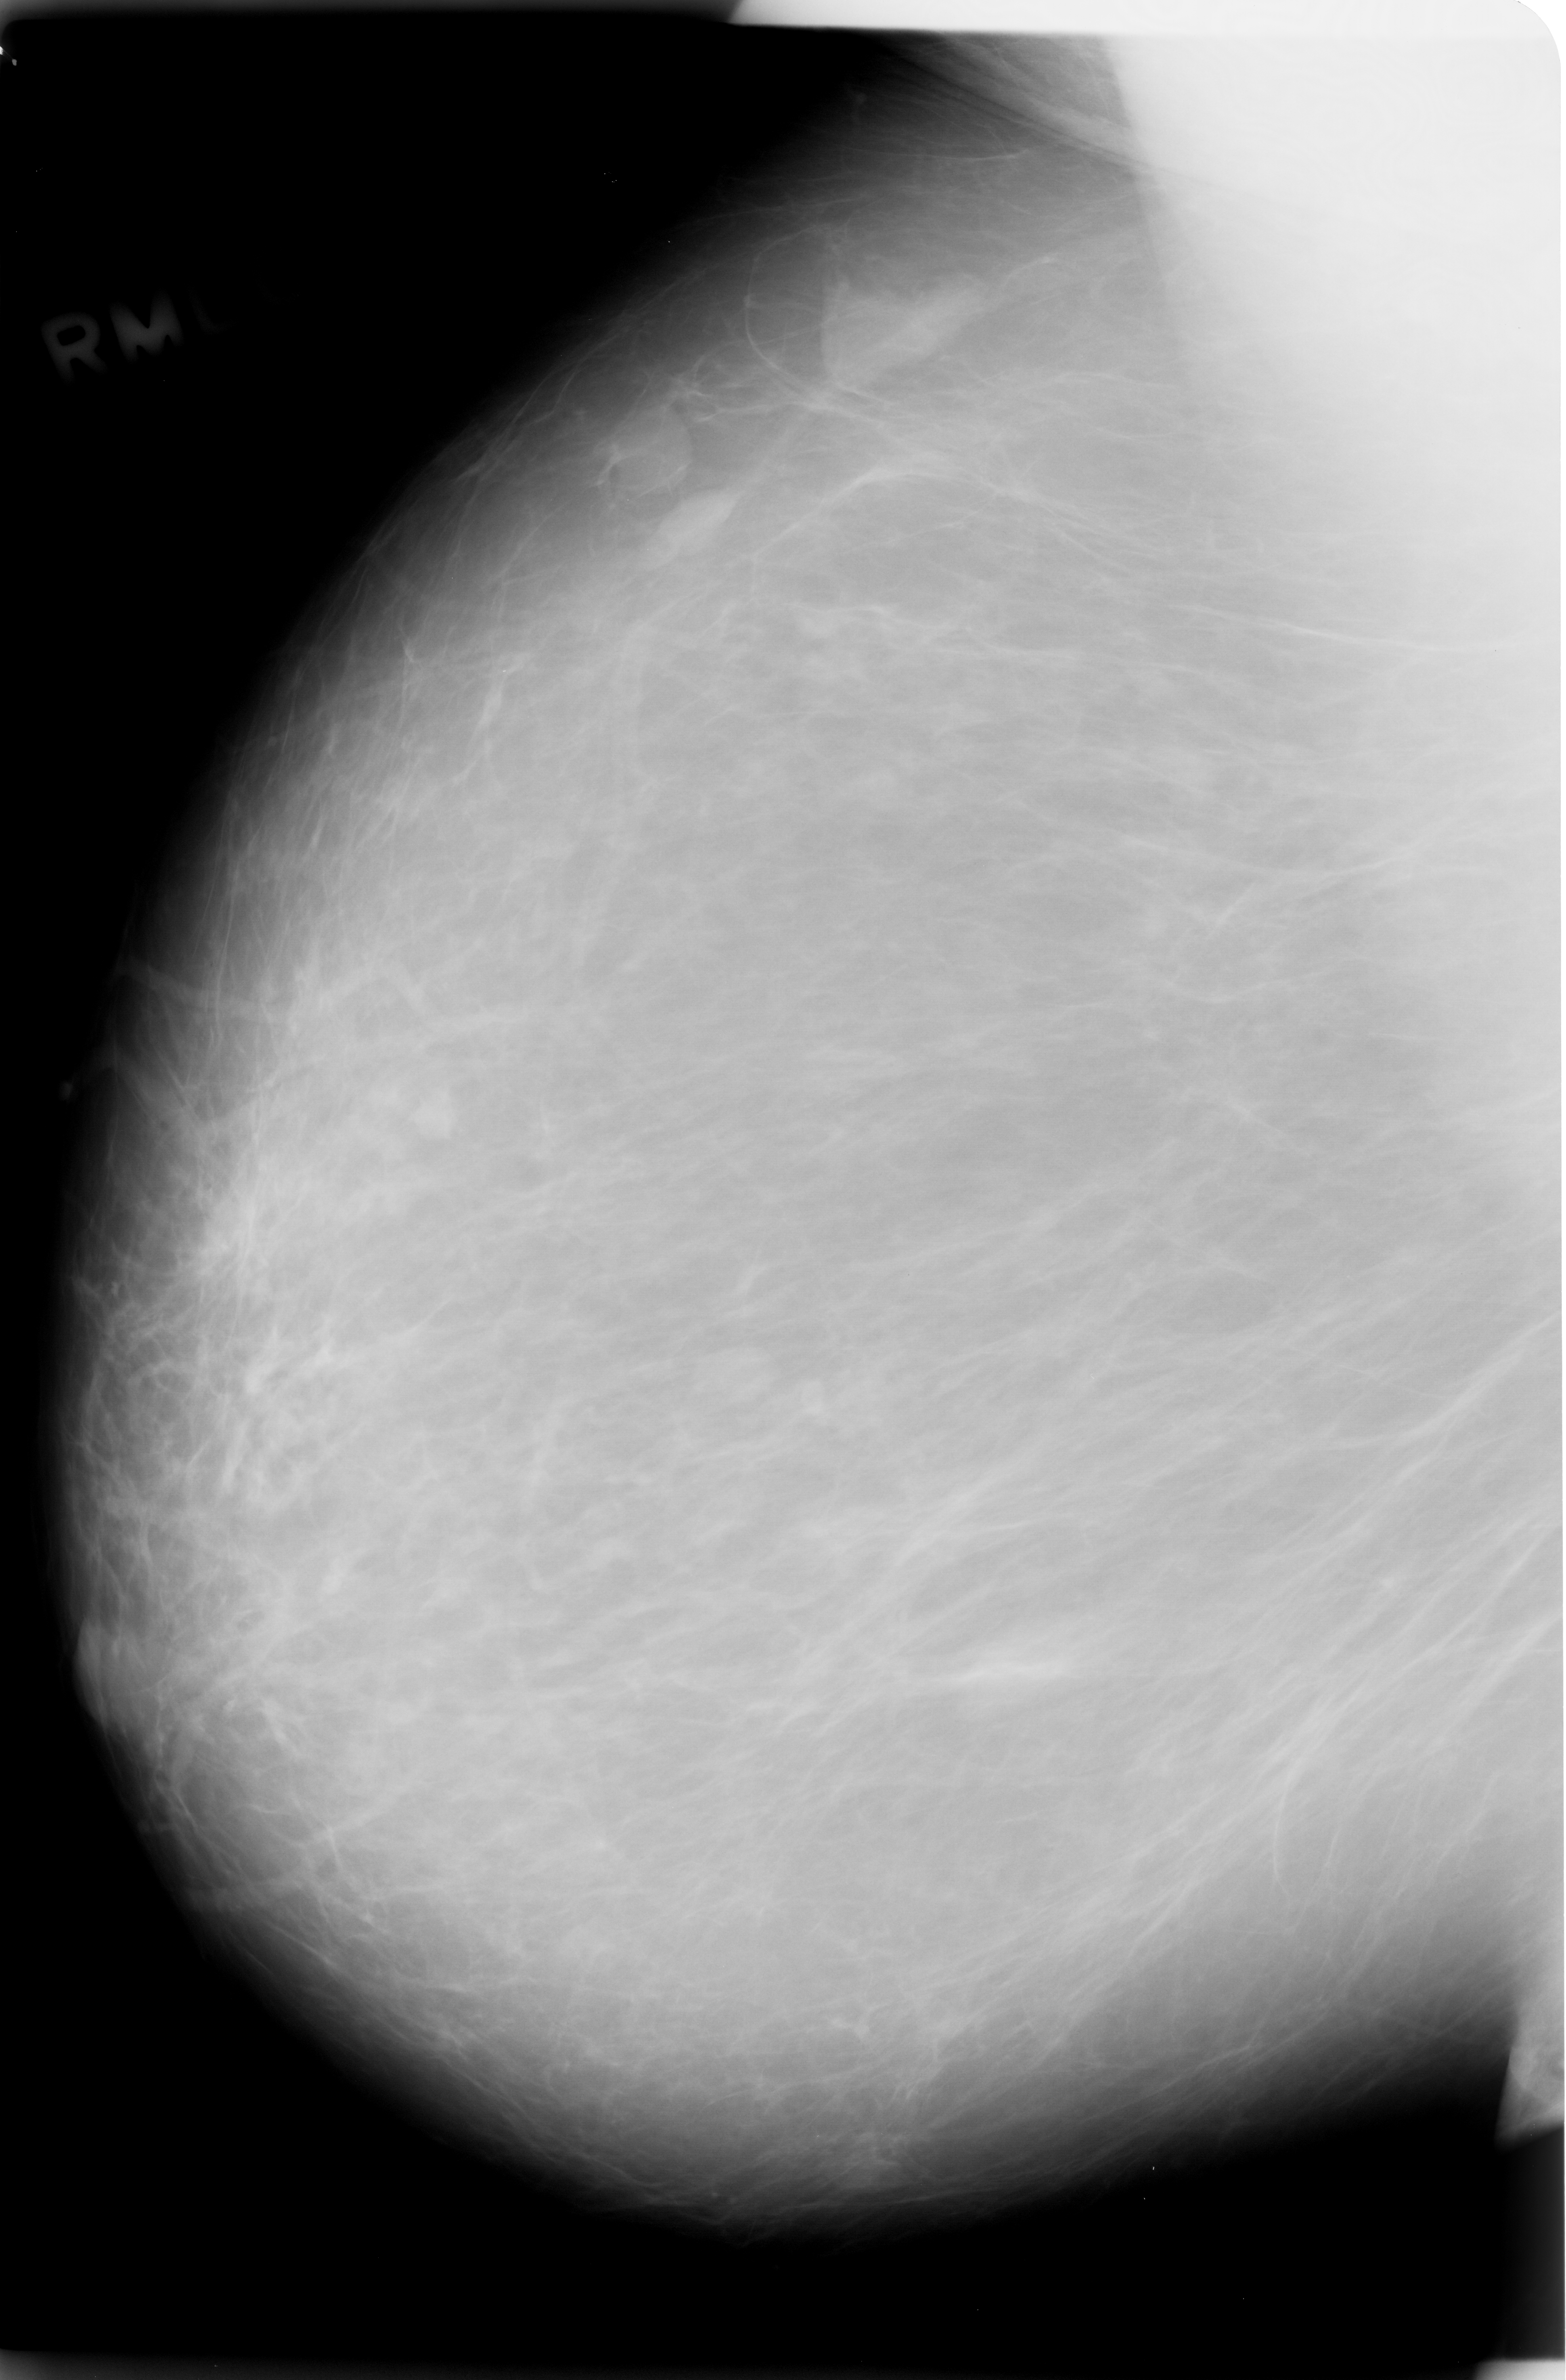
Mammogram (digitized film). Right breast. Mediolateral oblique (MLO) view. BI-RADS breast density category 1 (scale 1–4). 1566 × 2380 image matrix.
Expert-marked regions of interest on this film, with their recorded descriptors:
- Finding 1 of 6: mass, shape round, margins circumscribed; BI-RADS assessment category 2; subtlety rating 5 on a 1 (subtle) to 5 (obvious) scale; pathology (as recorded): benign: box from (x=408, y=1080) to (x=464, y=1140) px
- Finding 2 of 6: mass, shape round, margins circumscribed; BI-RADS assessment category 2; subtlety rating 5 on a 1 (subtle) to 5 (obvious) scale; pathology result (as recorded, not read from the image): benign: (x=616, y=428)–(x=741, y=568)
- Finding 3 of 6: mass, shape round, margins circumscribed; BI-RADS assessment category 2; pathology result (as recorded, not read from the image): benign: (x=682, y=1326)–(x=788, y=1425)
- Finding 4 of 6: mass, shape round, margins circumscribed; BI-RADS assessment category 2; subtlety rating 5 on a 1 (subtle) to 5 (obvious) scale; pathology (as recorded): benign: (x=813, y=2065)–(x=923, y=2186)
- Finding 5 of 6: mass, shape round, margins circumscribed; BI-RADS assessment category 2; pathology result (as recorded, not read from the image): benign: (x=835, y=273)–(x=961, y=384)
- Finding 6 of 6: mass, shape round, margins circumscribed; BI-RADS assessment category 2; pathology result (as recorded, not read from the image): benign: (x=937, y=1615)–(x=1102, y=1717)